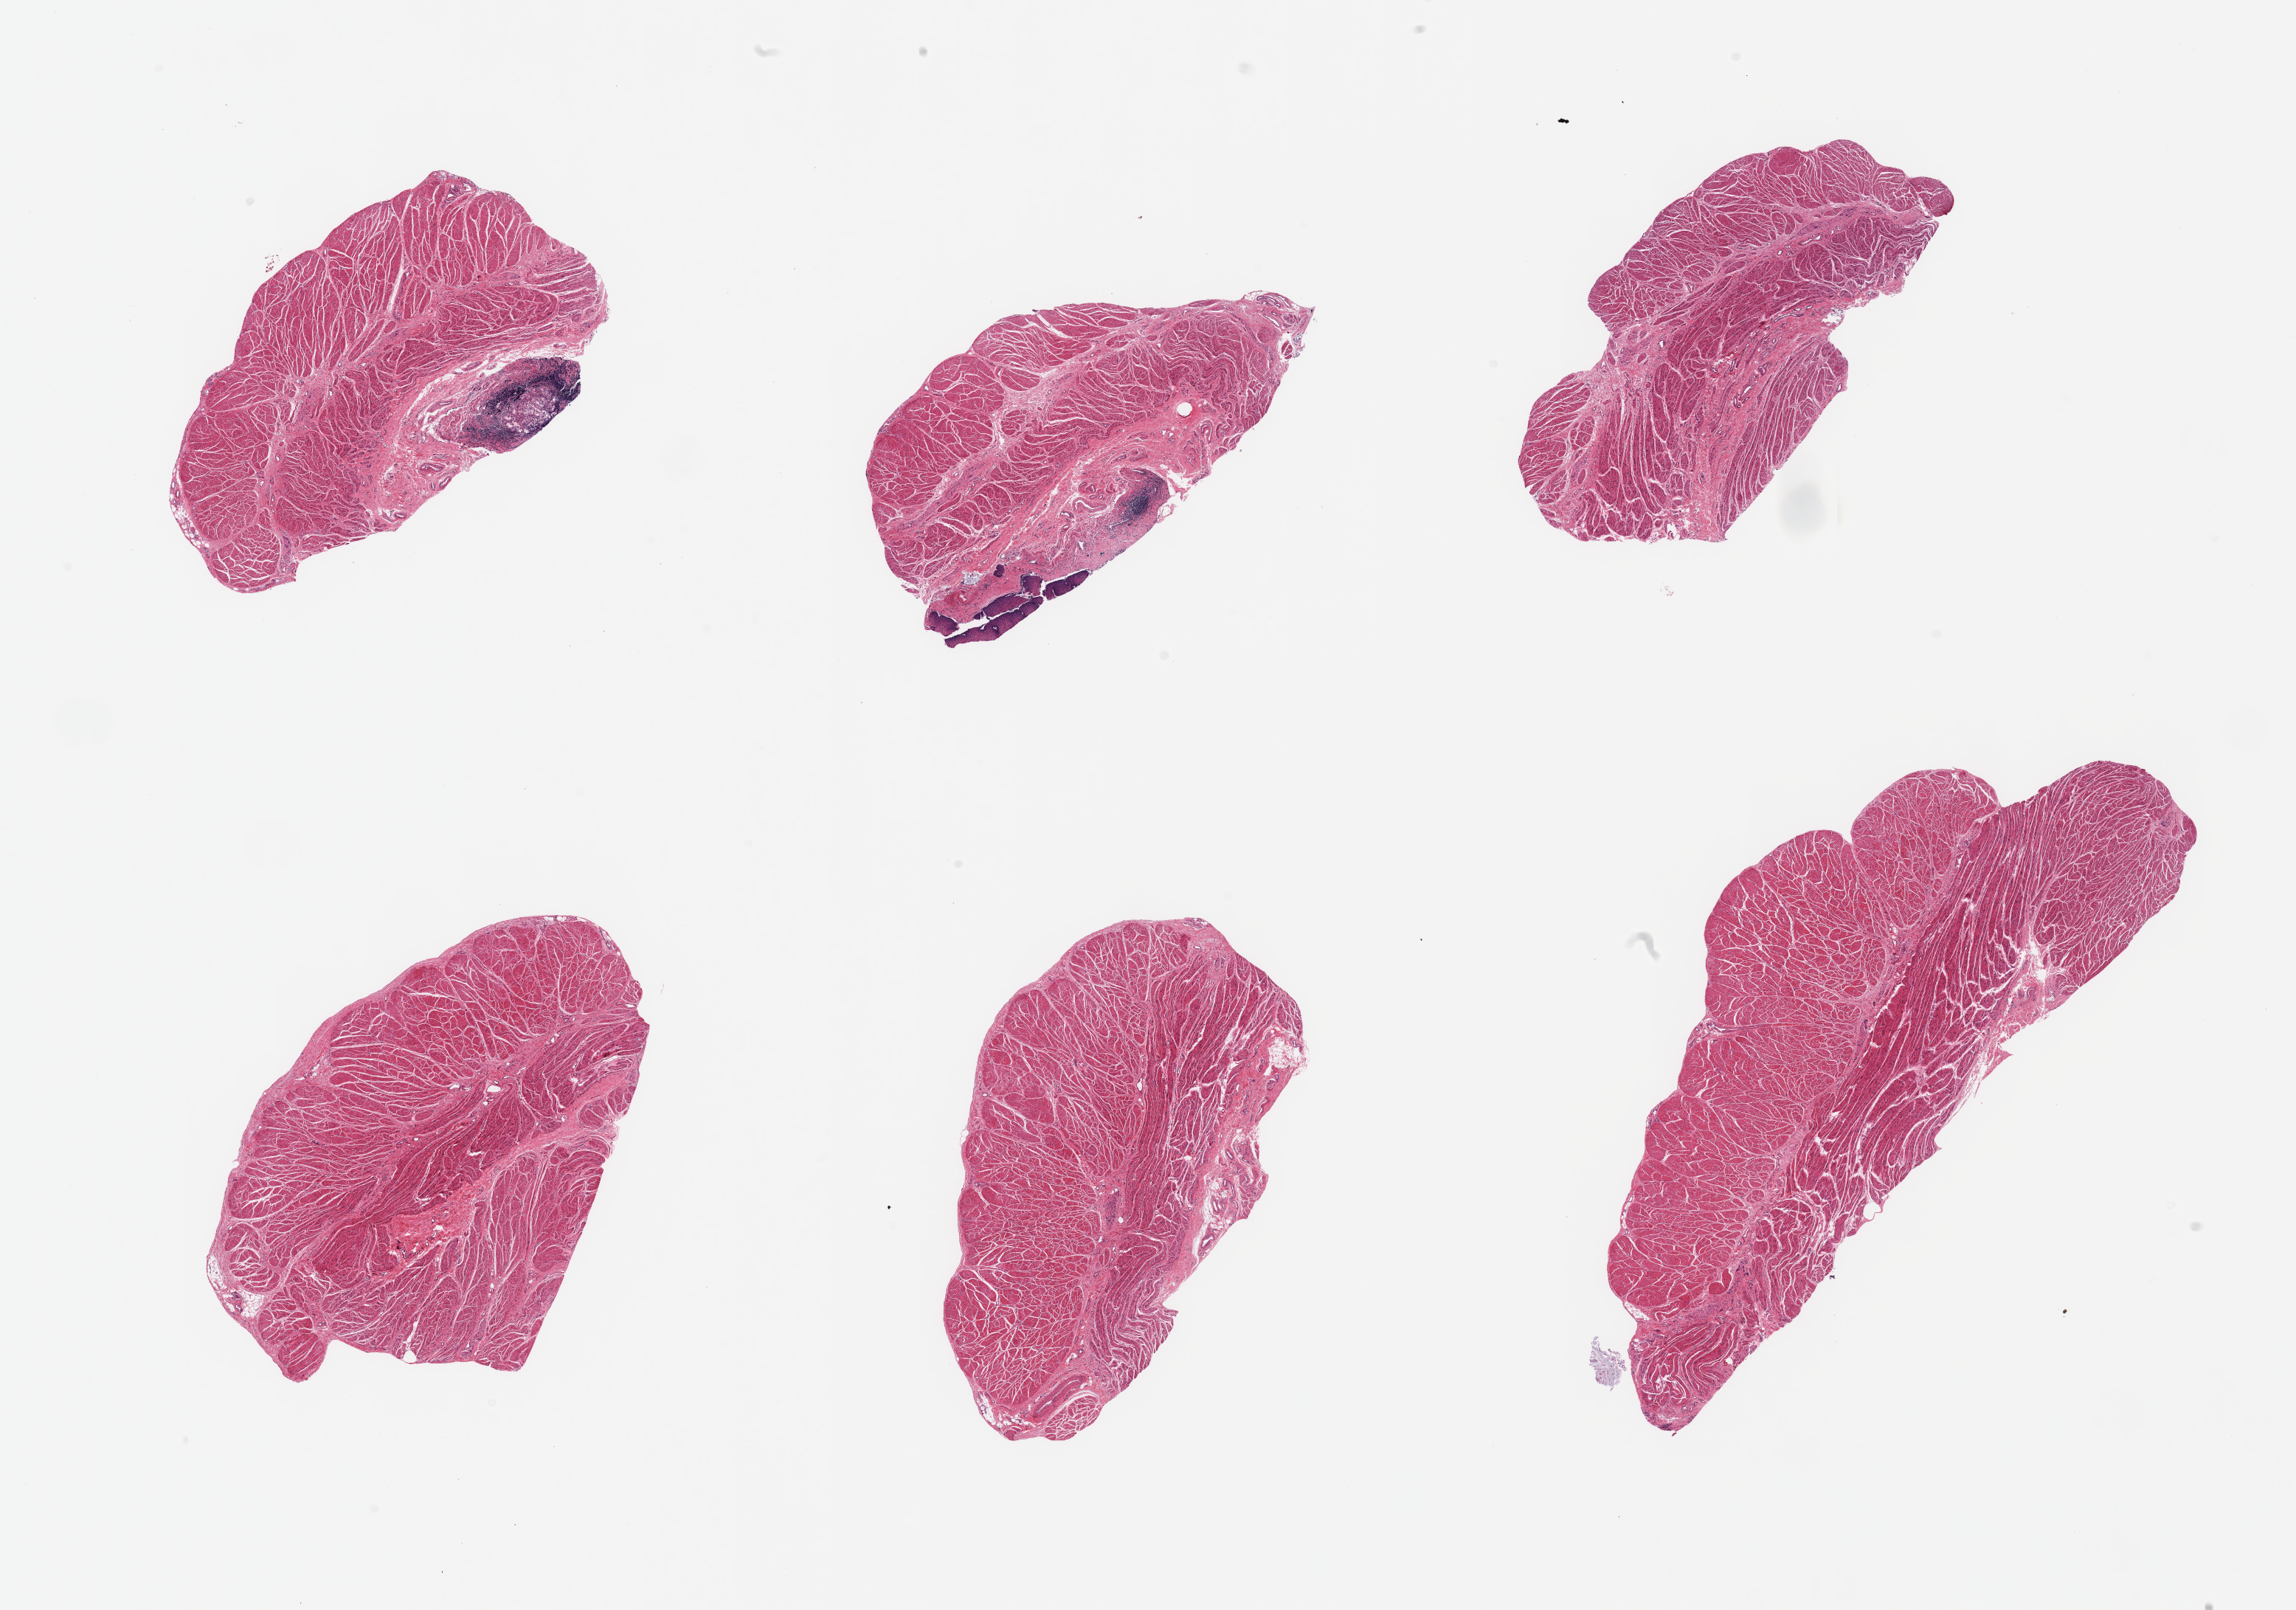
Digitized hematoxylin and eosin (H&E)-stained section, low-resolution overview of the scanned area, about 24.6 x 17.3 mm (from a 20x scan); PAXgene-fixed paraffin-embedded (PFPE) section; target tissue: gastroesophageal junction; tissue donor sample. Male donor.
- pathologist's review note for this sample: 6 pieces, confirmed target muscularis; trace mucosa/gland